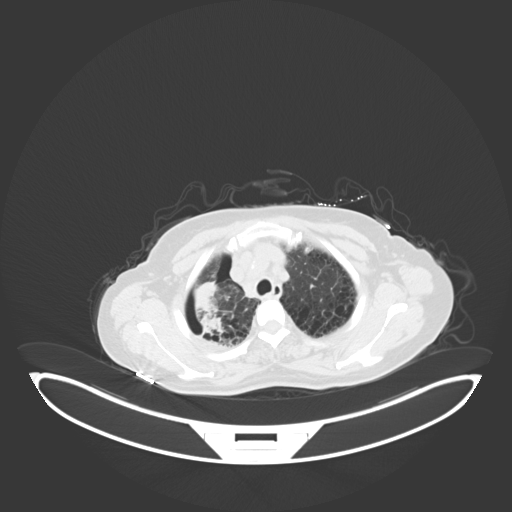
Chest CT, one axial slice; slice 52 of 69 in the series (ordered by position); reconstruction kernel B30f; lung window (W 1500 / L -600 HU); 3 mm slice thickness; 512 × 512 image matrix. Patient: female, 64 years. From the clinical record (not read from this slice): clinical TNM (as recorded): T3 N3 M0.
Structures marked on this image (bounding box drawn by a radiologist):
- lung tumour (recorded histology: squamous cell carcinoma): bounding box [x1, y1, x2, y2] px = [190, 282, 230, 345]